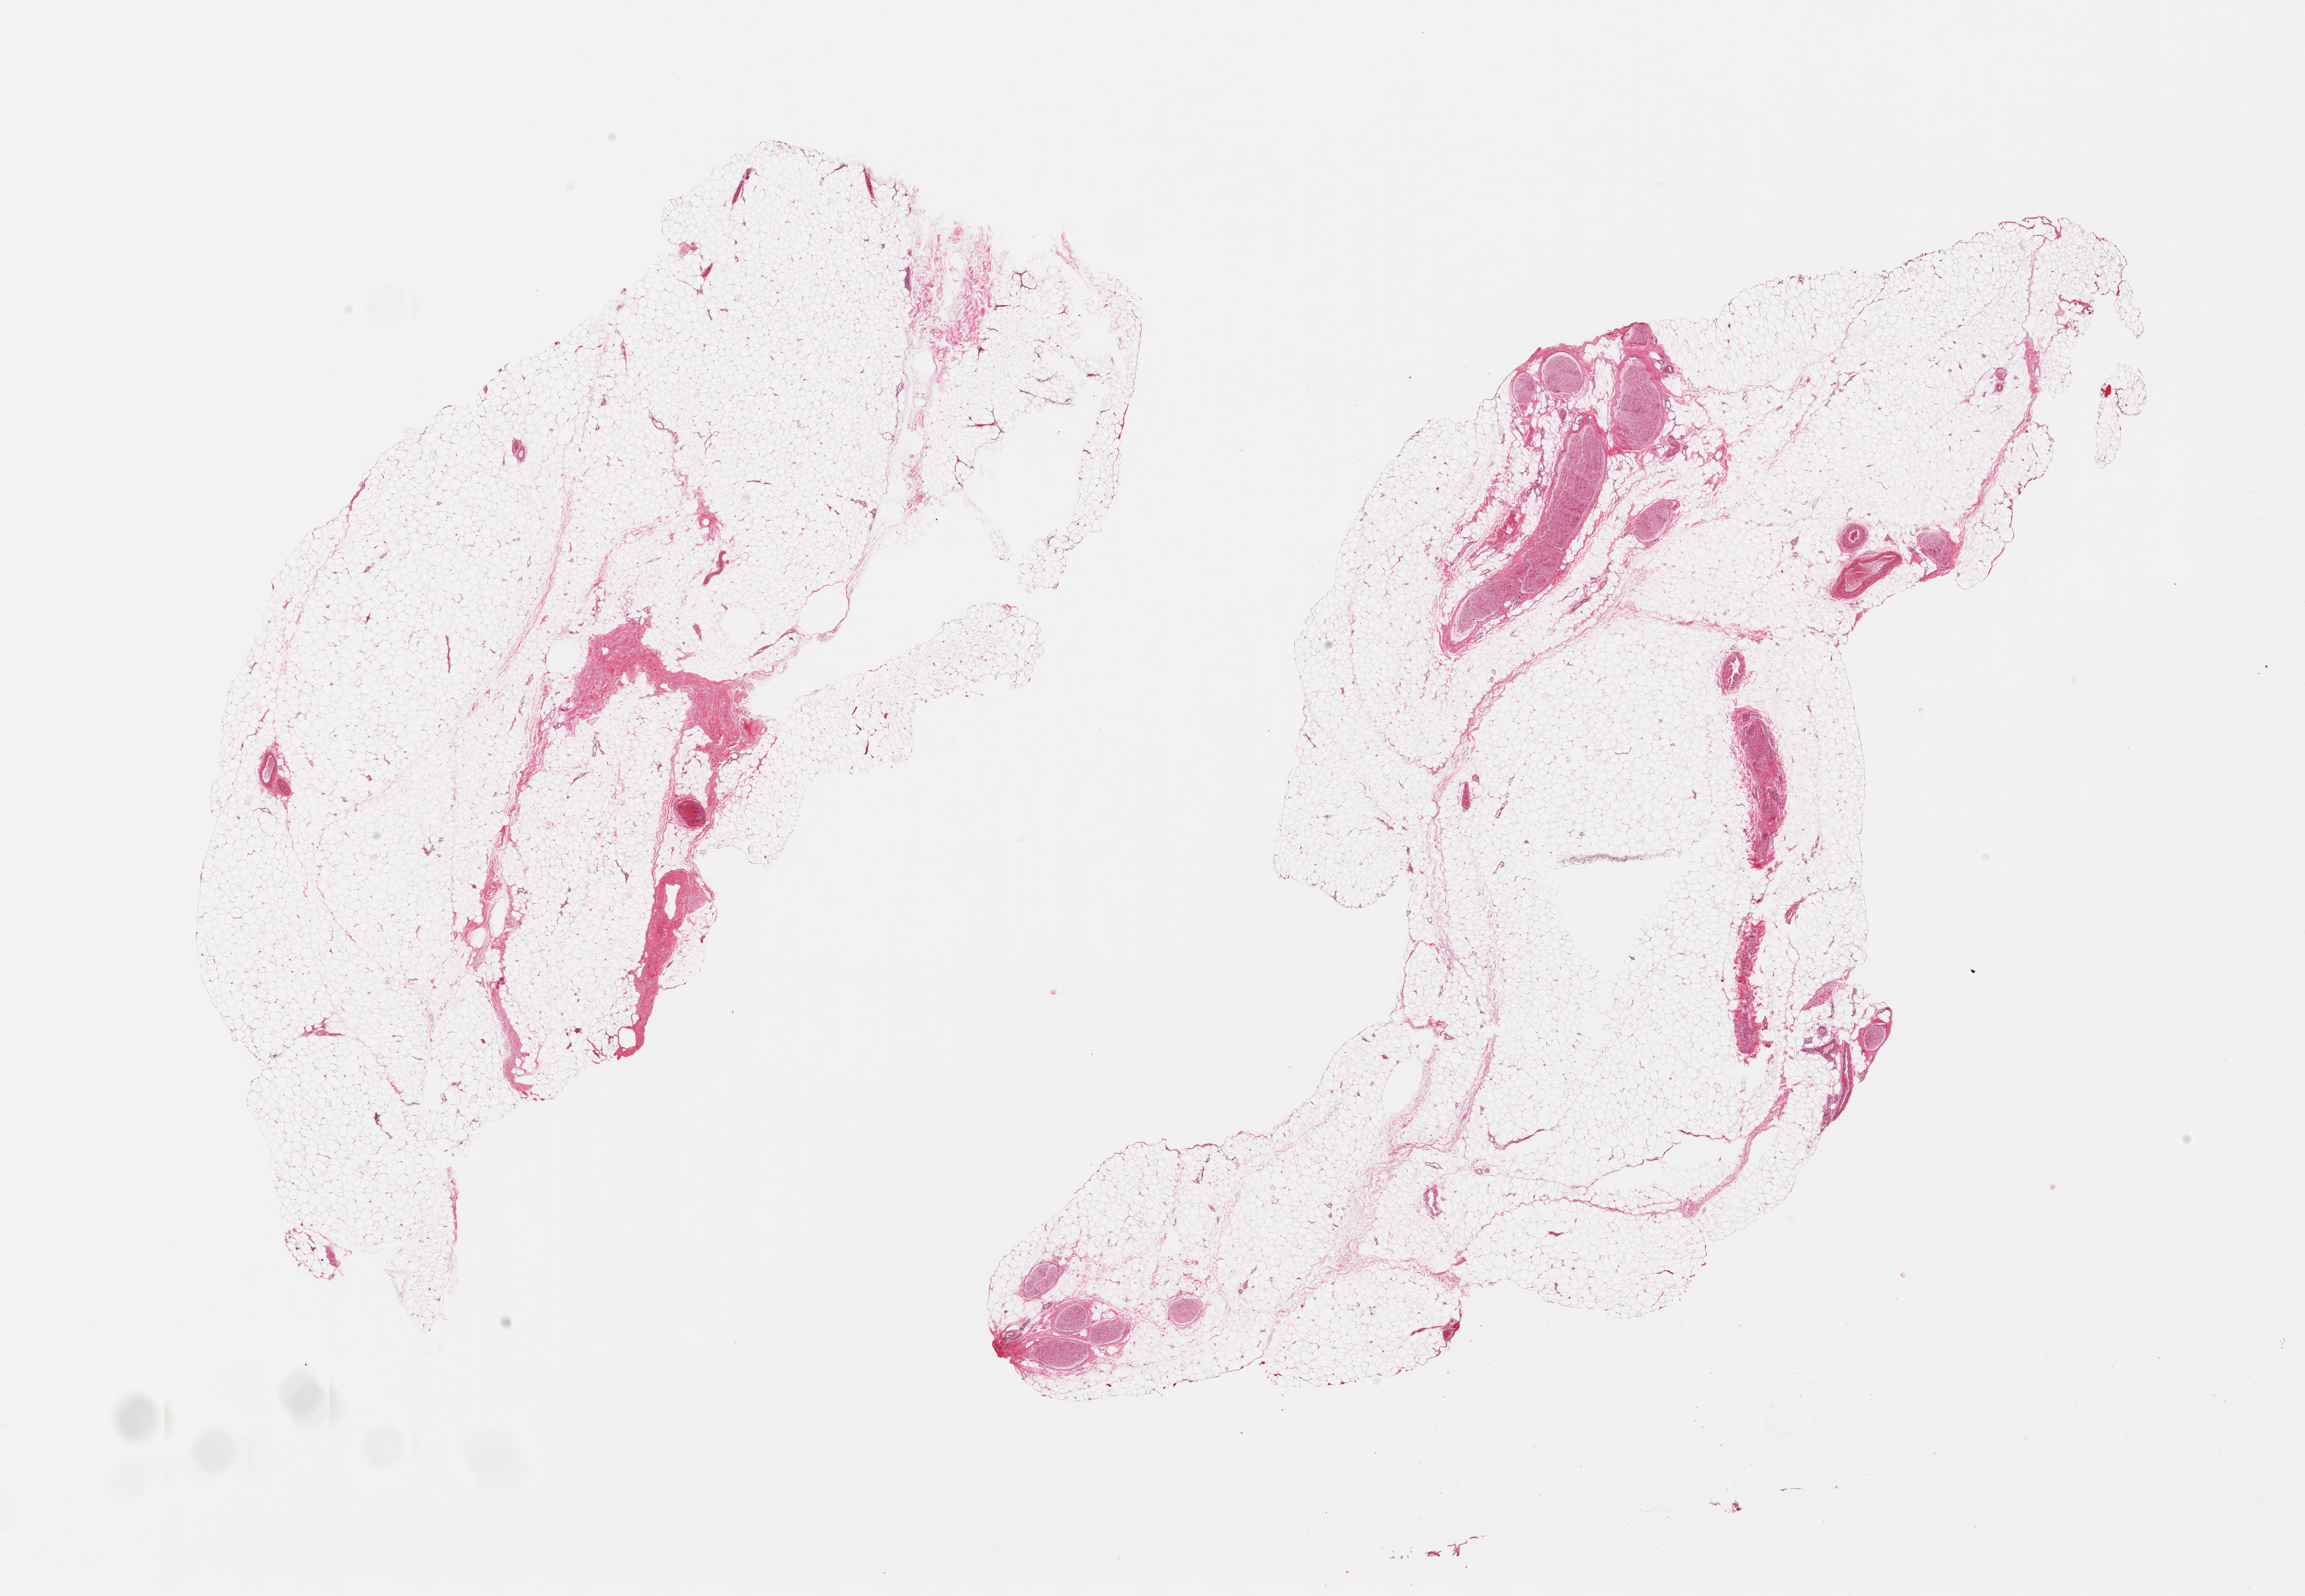
Hematoxylin and eosin (H&E) whole-slide image — shown as a low-resolution overview of the whole scanned area (about 27.6 x 19.1 mm), PAXgene-fixed paraffin-embedded (PFPE) section, sampled site (target tissue): adipose tissue, donor tissue sample. Male donor.
- review note (as recorded): 2 pieces, ~10% fascia, peripheral nerve, or vascular elements